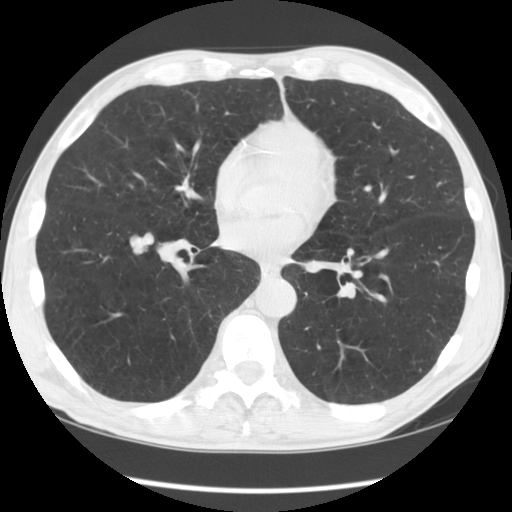
Low-dose screening chest CT, one axial slice. Position 52 of 135 along the scan axis. Reconstruction kernel STANDARD. 120 kVp. Lung window (W 1500 / L -600 HU). 2.5 mm slice thickness. 512 × 512 image matrix.
Structures marked on this image (manually delineated by an expert):
- lesion 1 (tumor, lower lobe of right lung): bounding box <130,233,154,255> (left, top, right, bottom; pixels)